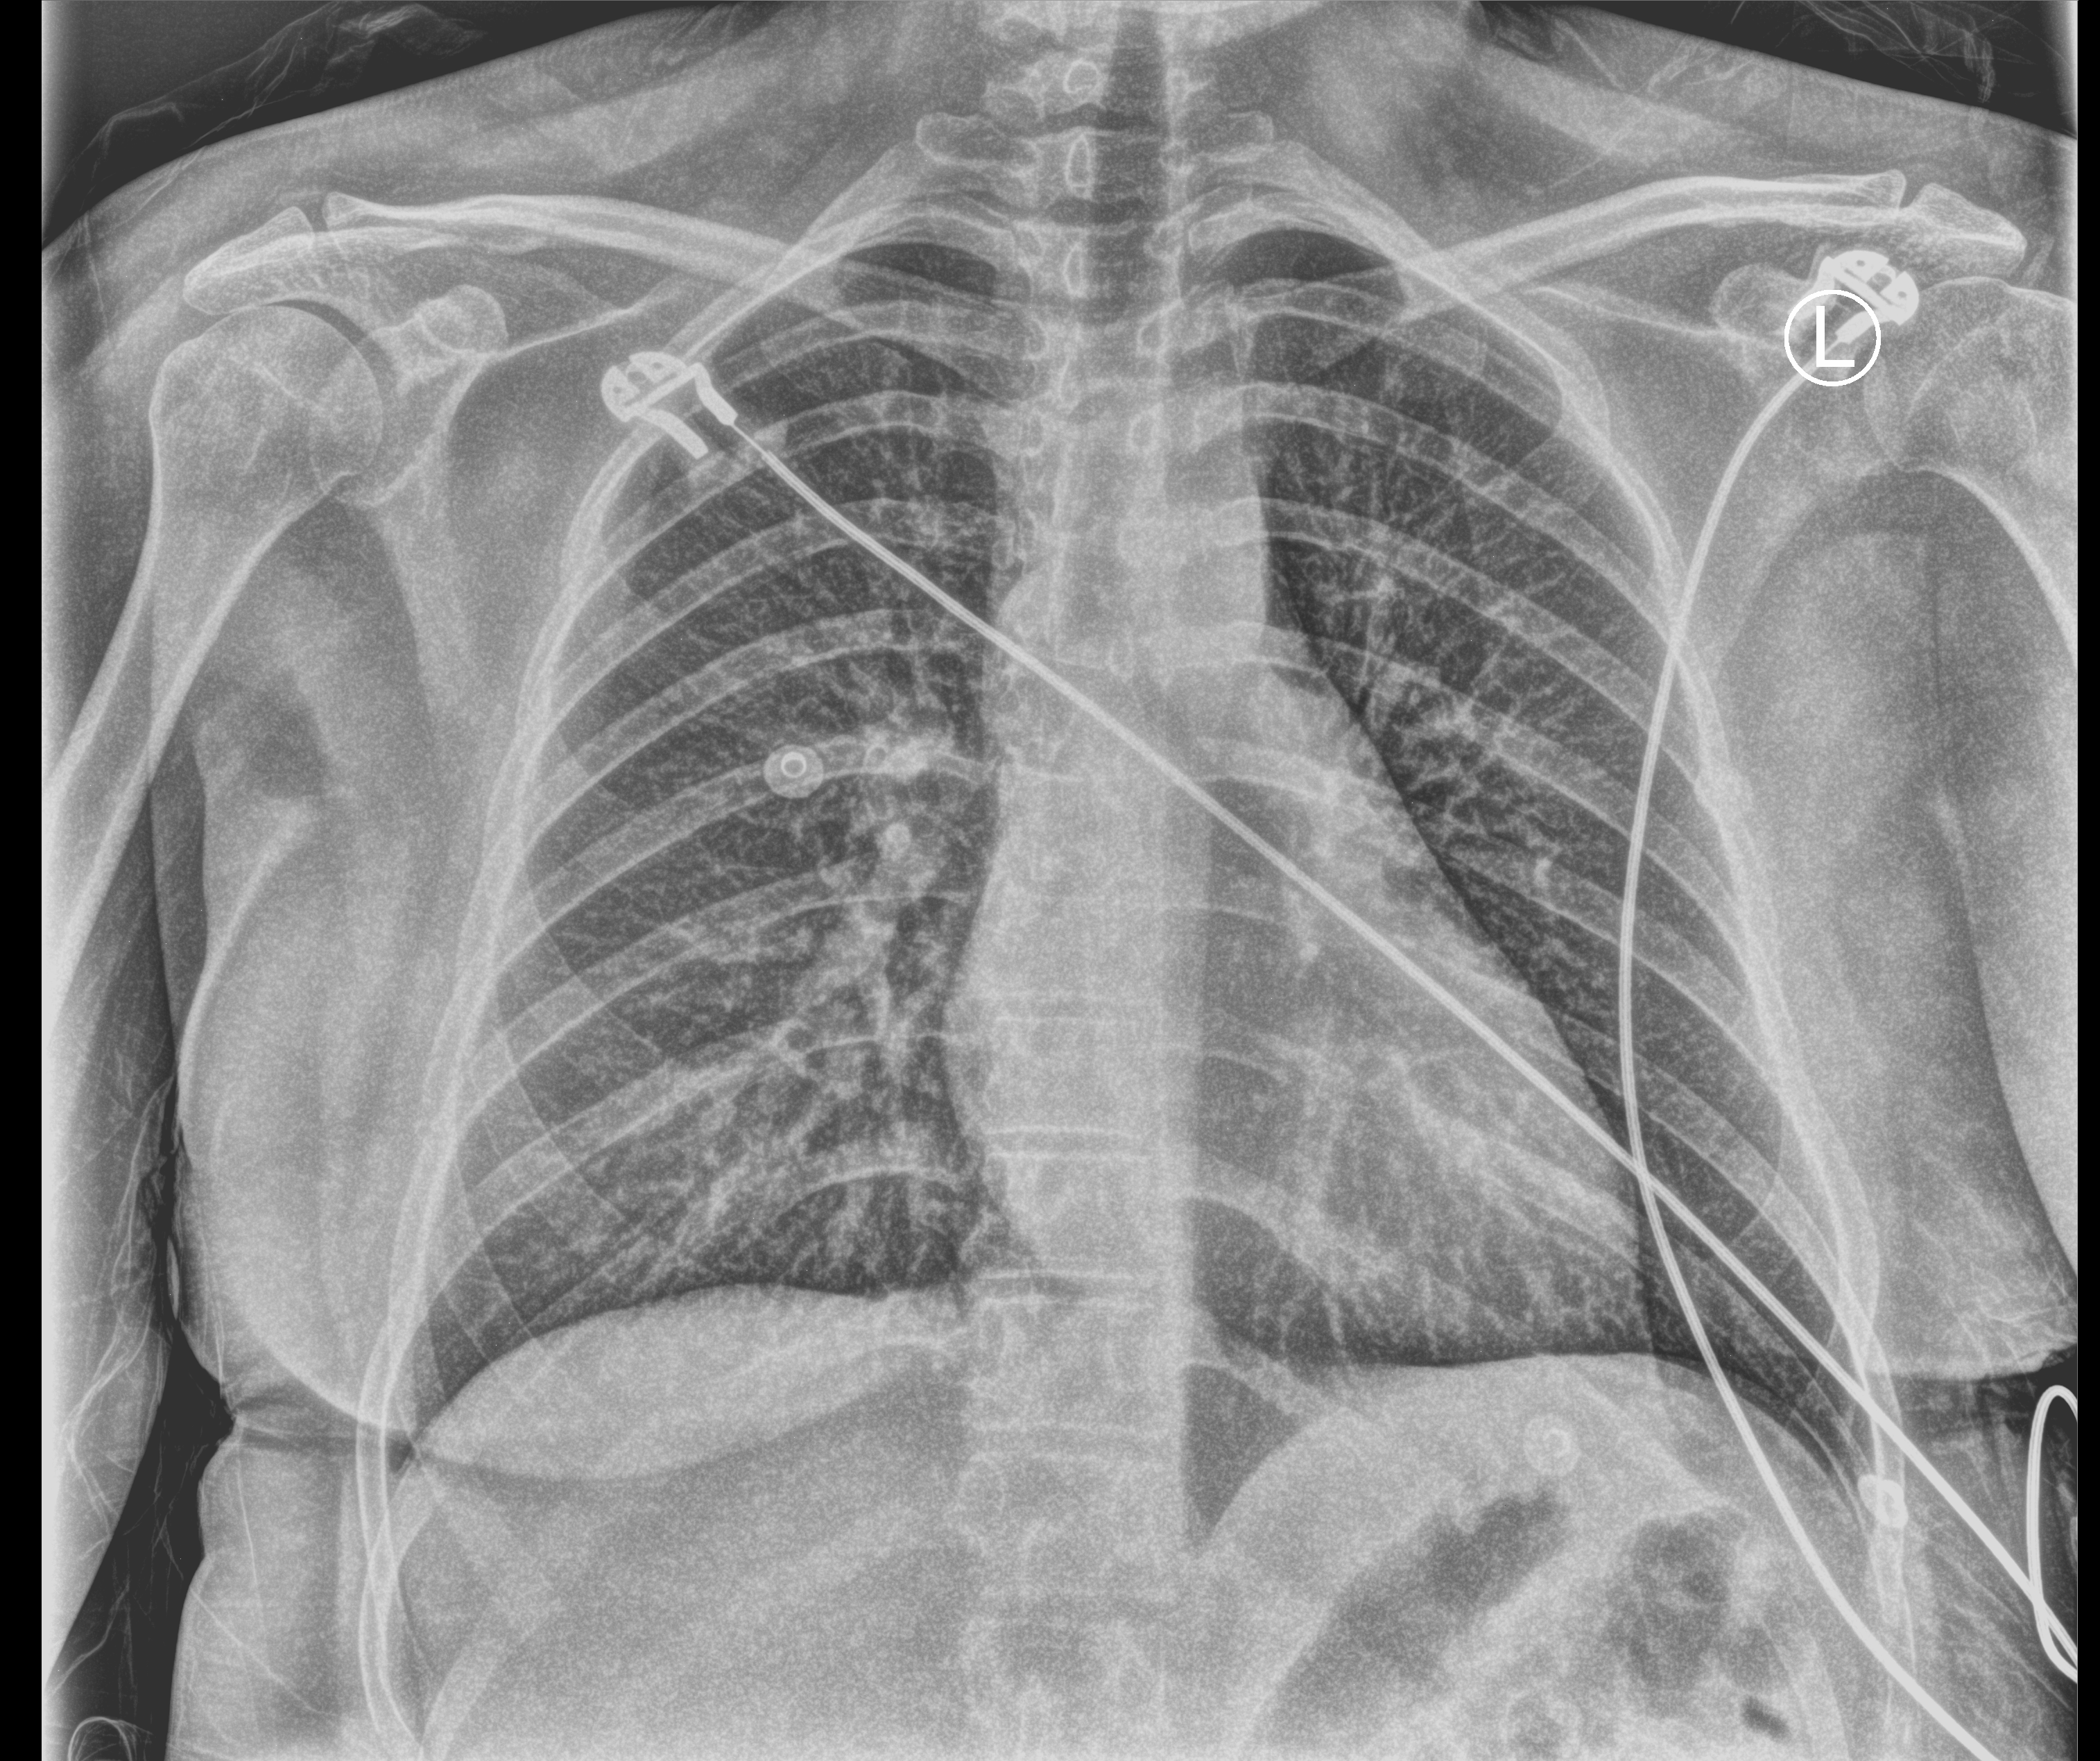
Bedside chest radiograph (computed radiography); anteroposterior (AP) projection. Patient hospitalised with COVID-19; female, aged 18–59 years.
Hospital-stay facts (about this admission, not read from this image; timing relative to this image not recorded):
- hypertension (admission record): no